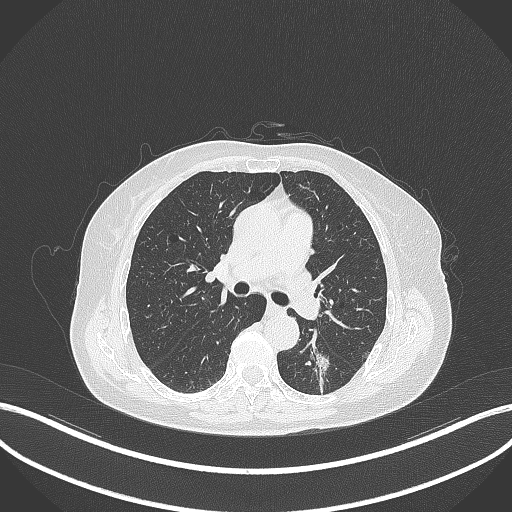
Chest CT, one axial slice; position 177 of 352 along the scan axis; reconstruction kernel B70f; 120 kVp; lung window (W 1500 / L -600 HU); 1 mm slice thickness; 512 × 512 image matrix, field of view 400 × 400 mm. Patient: female, 70 years. From the clinical record (not read from this slice): clinical TNM (as recorded): T1c N0 M0.
Outlined on this slice (rectangle marked by the reading radiologist):
- lung tumour (recorded histology: adenocarcinoma): bounding box <302,340,331,382> (left, top, right, bottom; pixels)